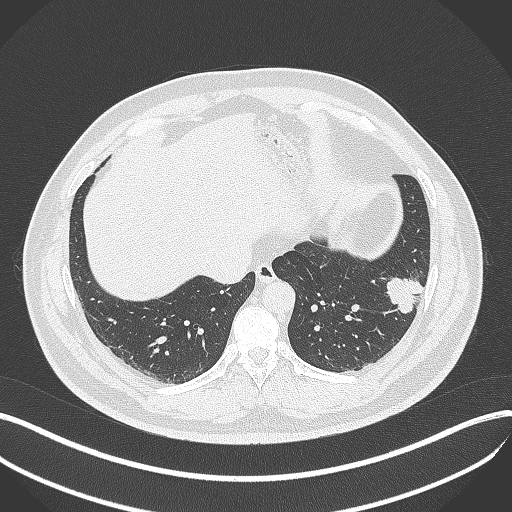
Chest CT, one axial slice; position 119 of 429 along the scan axis; reconstruction kernel B70f; lung window (W 1500 / L -600 HU); 1 mm slice thickness; 512 × 512 image matrix, field of view 400 × 400 mm. Patient: male, 39 years. Case-level facts recorded for this patient, not image findings: clinical TNM (as recorded): T2a N0 M0; histopathological grade: G2-3.
Annotated regions visible in this slice (rectangle marked by the reading radiologist):
- lung tumour (recorded histology: adenocarcinoma): bounding box [x1, y1, x2, y2] px = [382, 271, 425, 321]